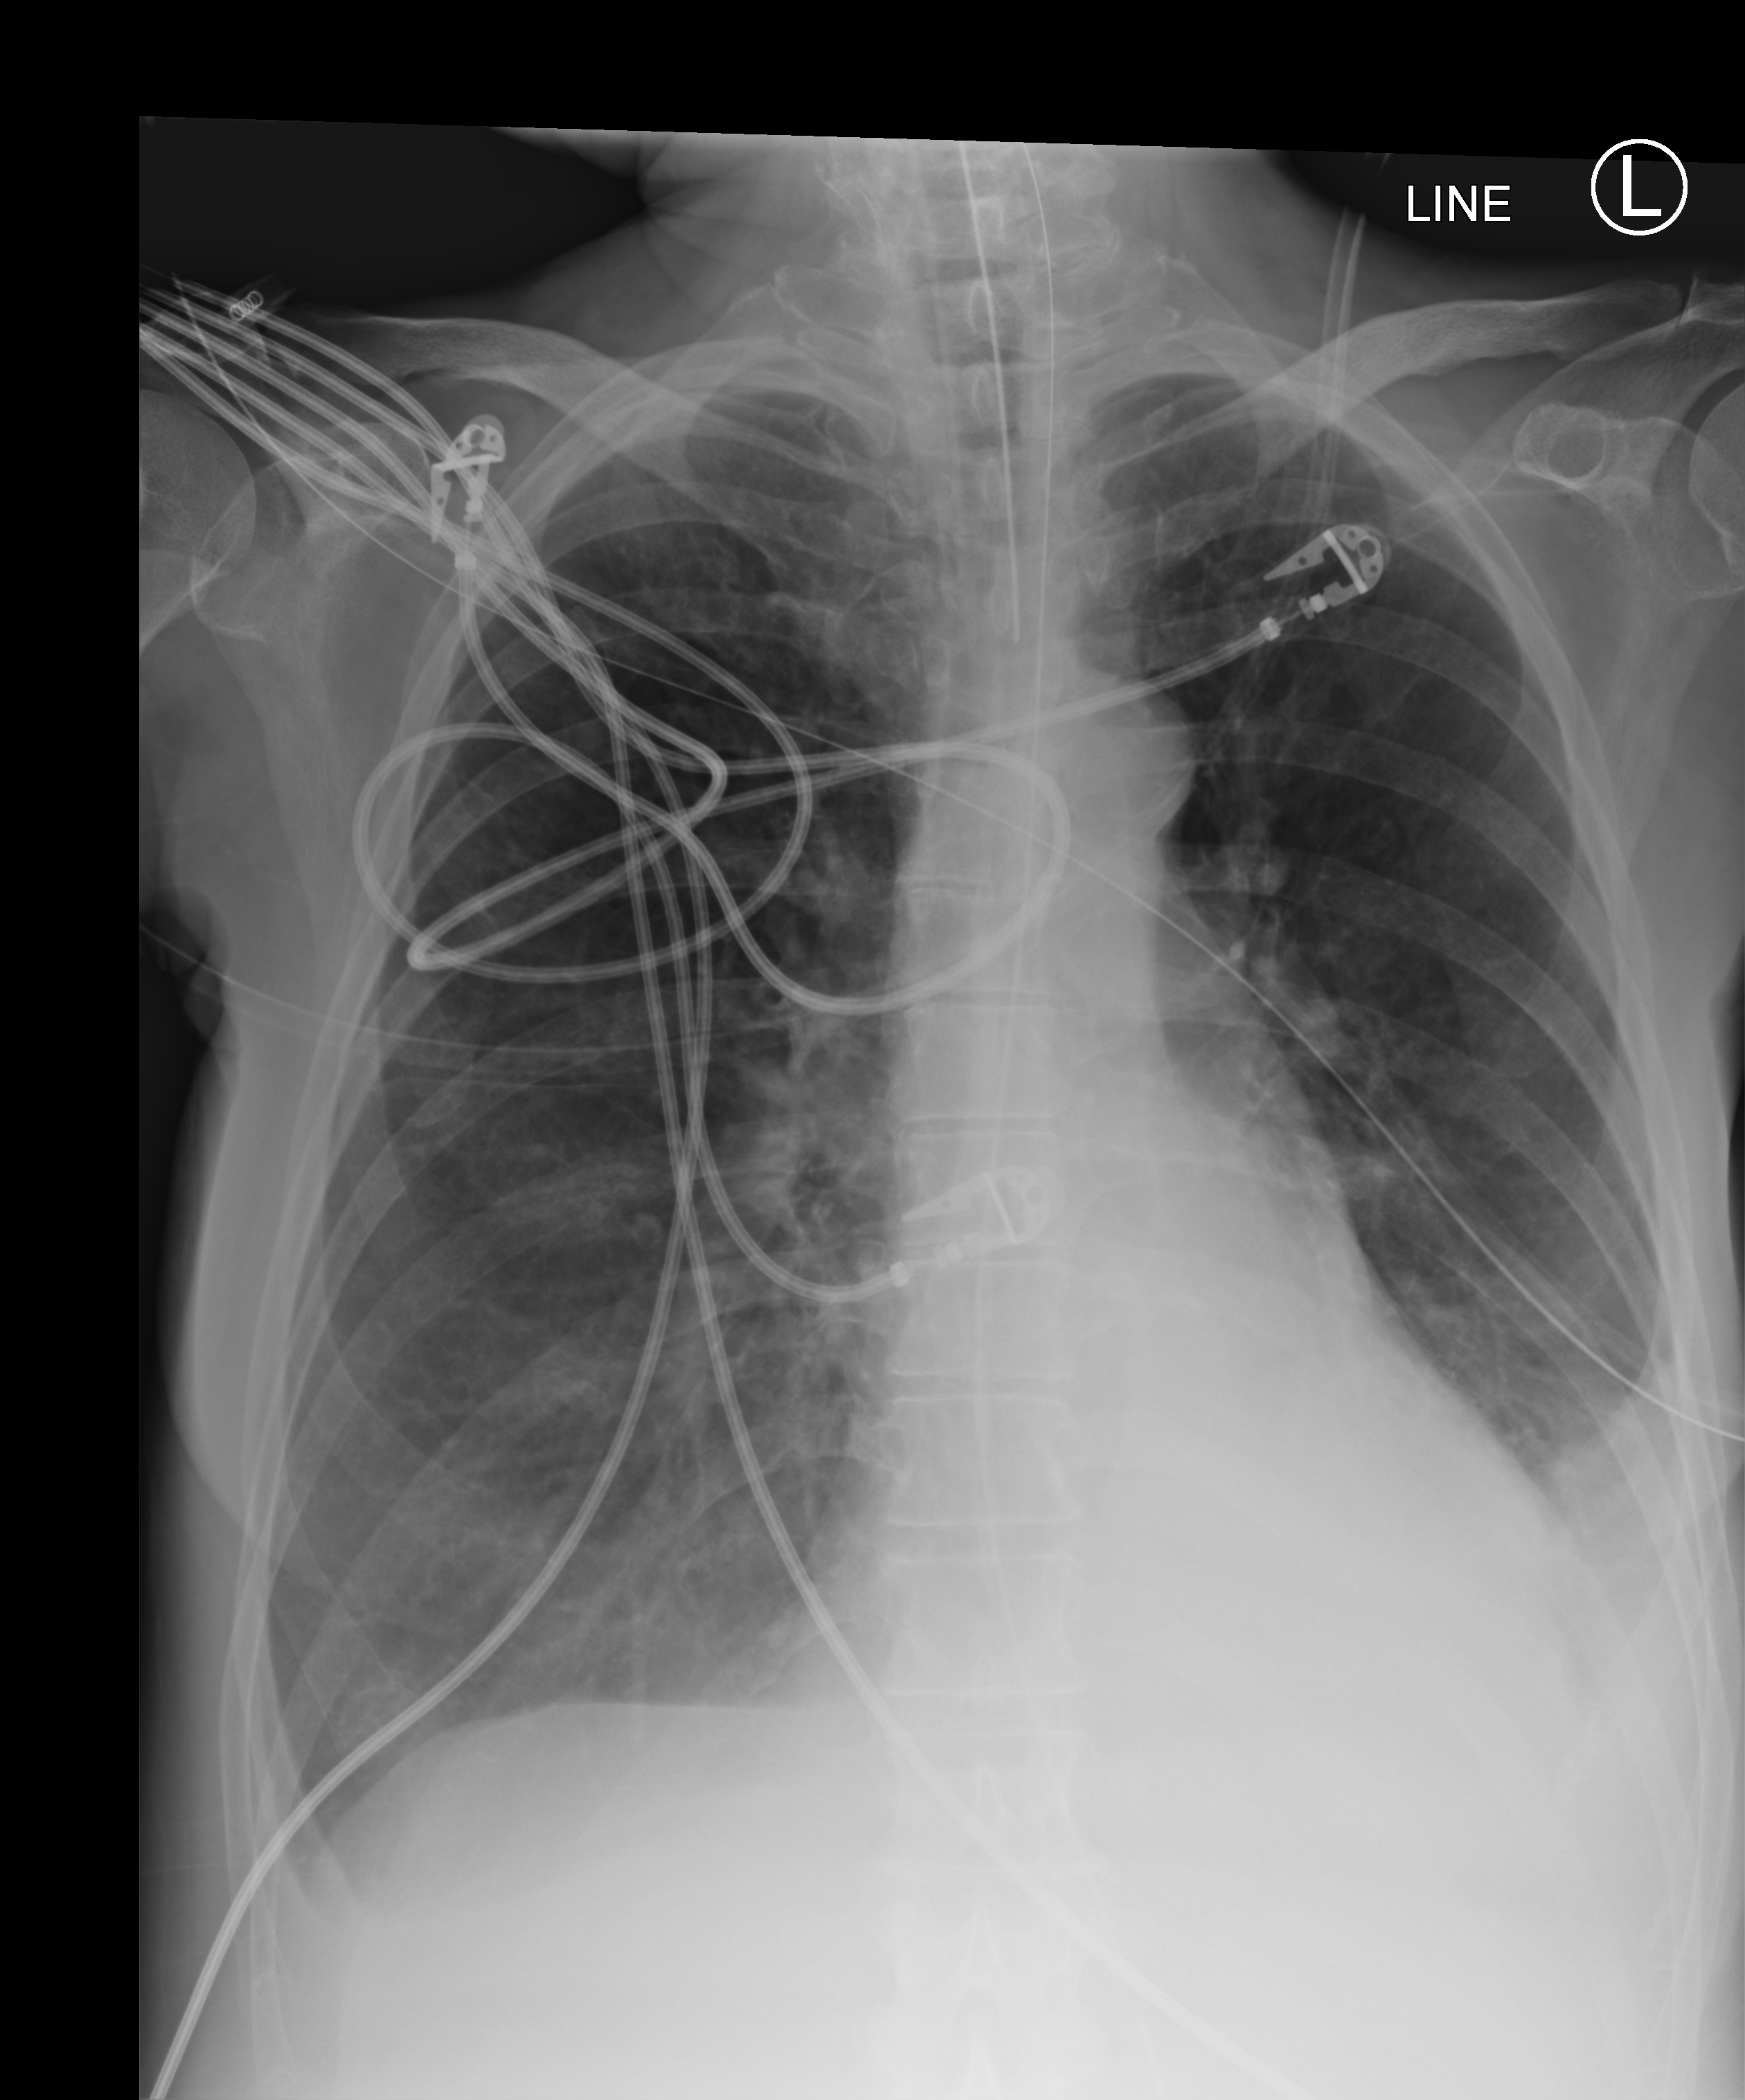
Bedside chest radiograph (computed radiography), anteroposterior (AP) projection. Patient hospitalised with COVID-19; female, aged 60–74 years.
Admission-level facts for this patient (not findings on this image; timing relative to this image not recorded):
- mechanically ventilated during this hospital stay: yes
- admitted to intensive care during this hospital stay: yes